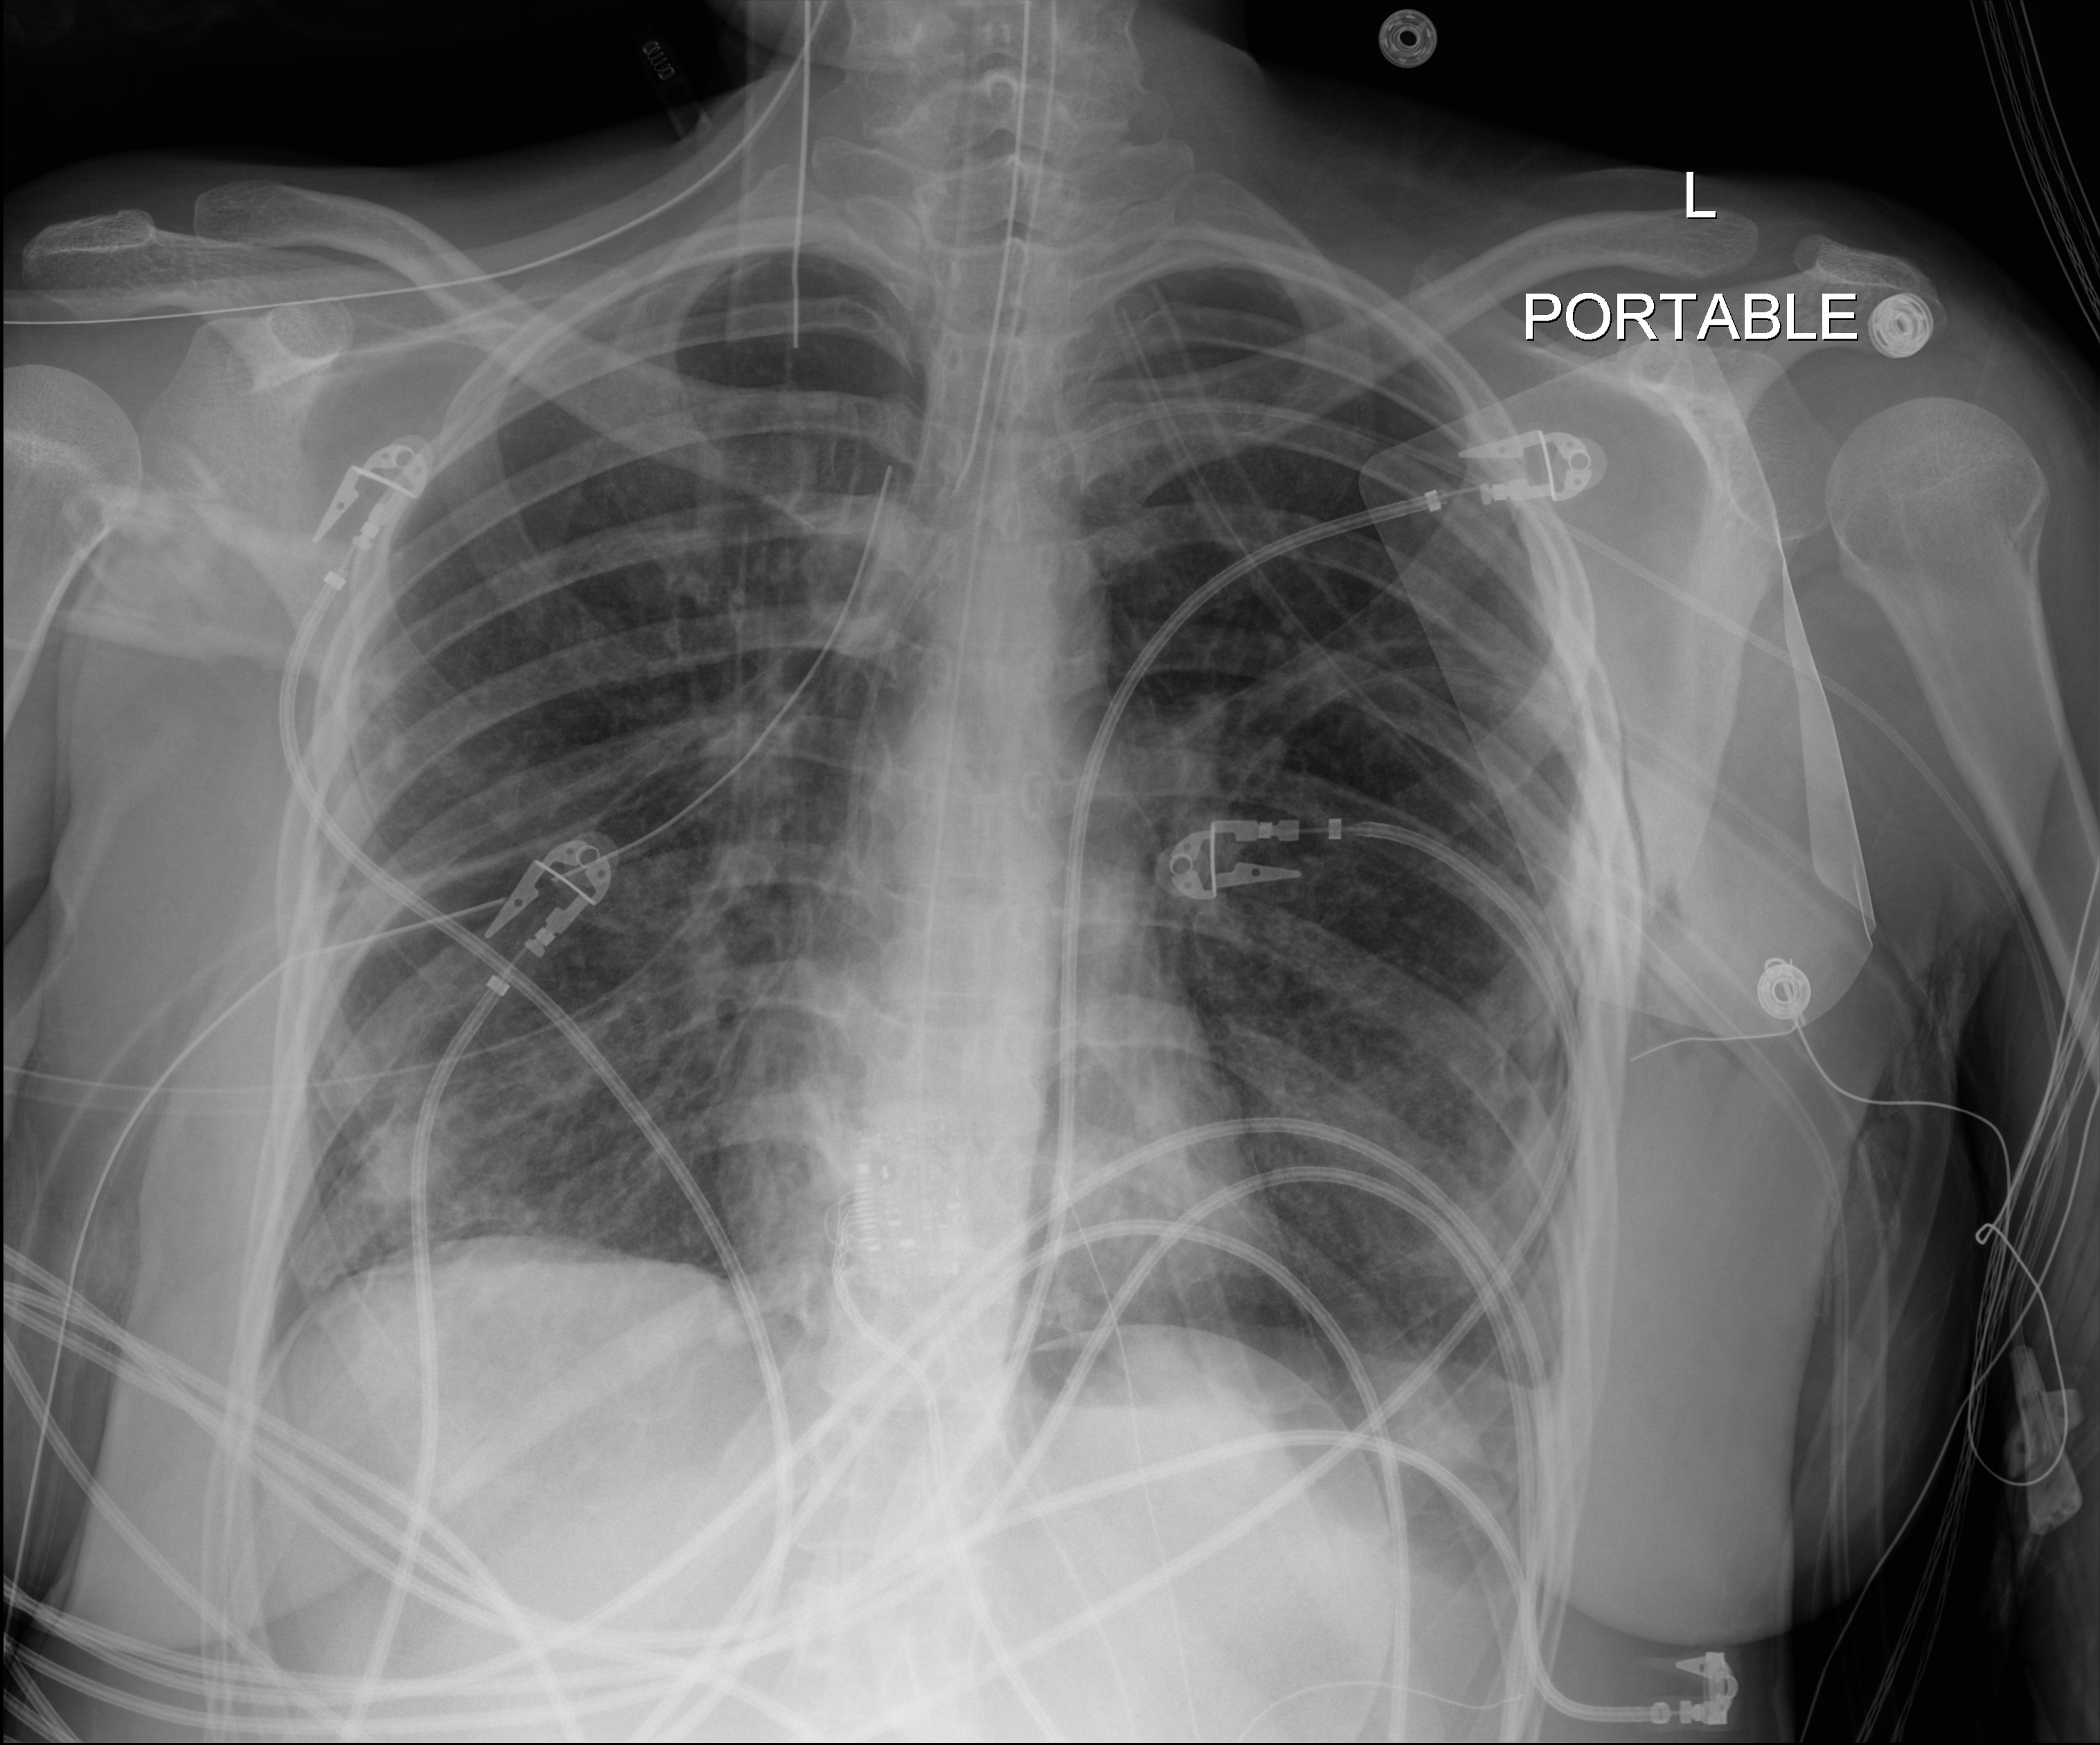
Portable chest radiograph; anteroposterior (AP) projection. Patient hospitalised with COVID-19, aged 18–59 years.
From the hospital-stay record, not from the radiograph (when in the stay this image was taken is not recorded): hypertension (admission record): no; admitted to intensive care during this hospital stay: yes.